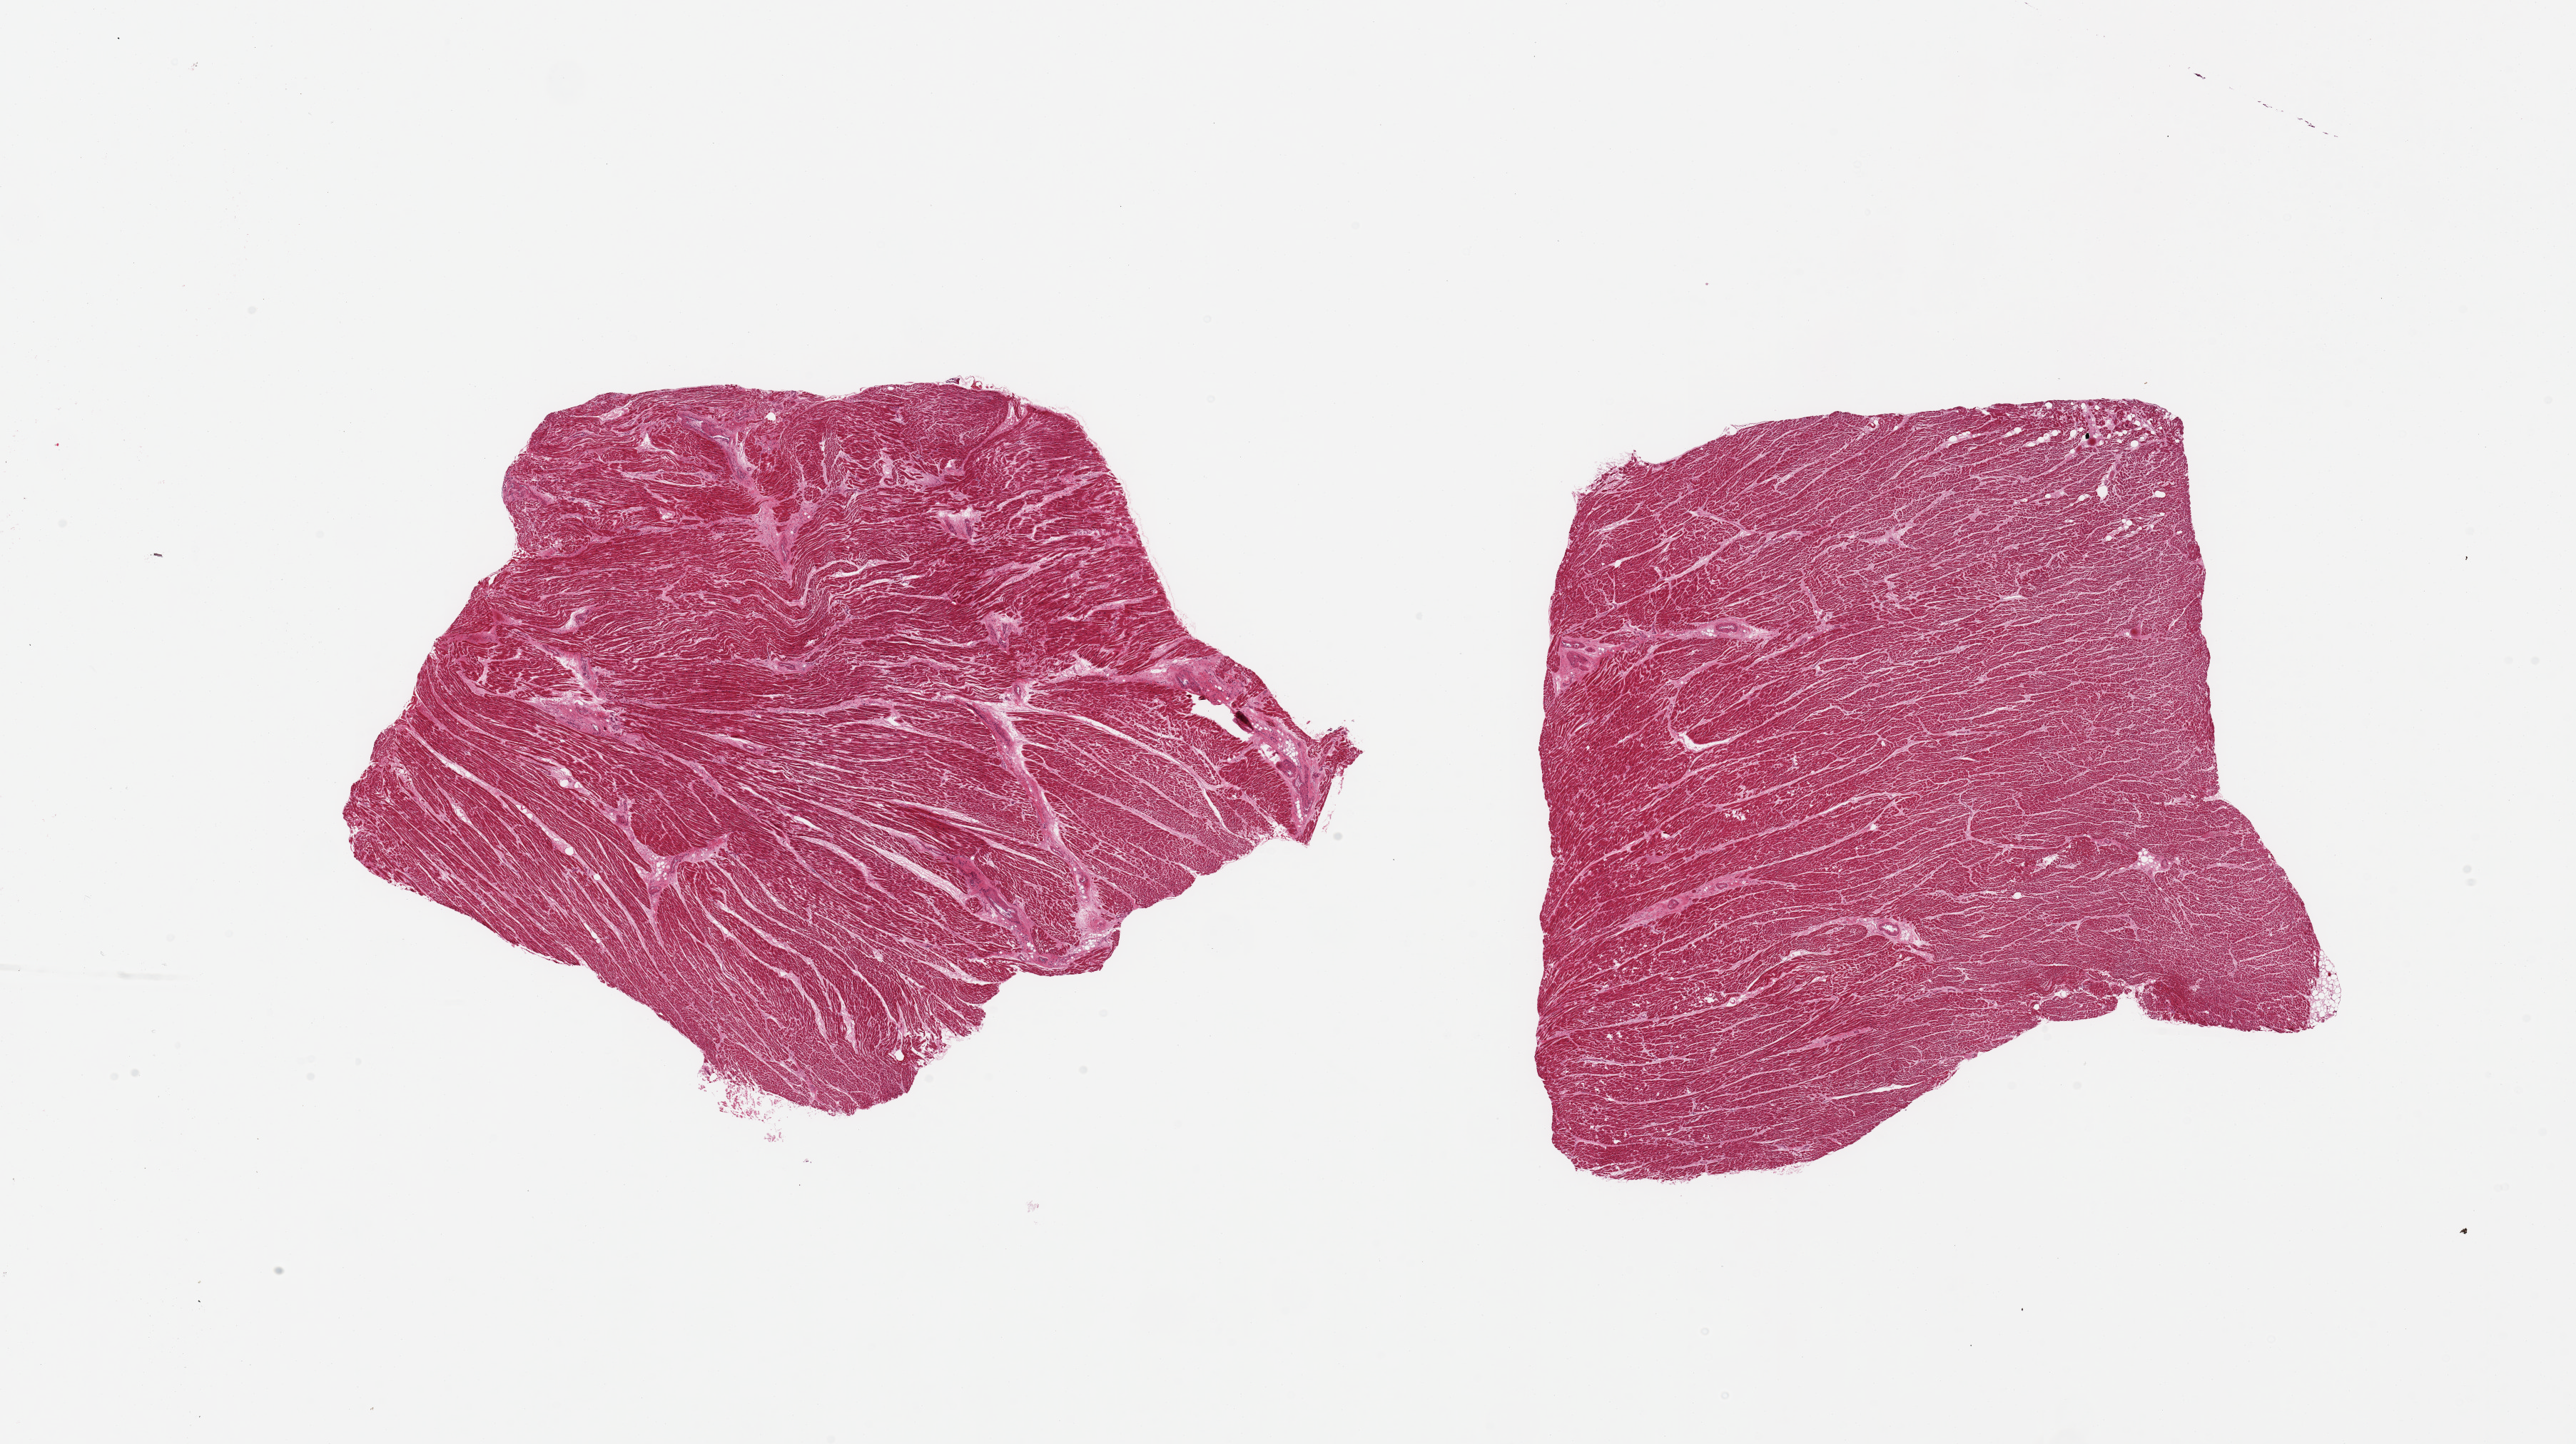
Haematoxylin and eosin whole-slide image — whole scanned area (about 28.5 x 16.0 mm, acquisition: 20x scan) shown as a low-resolution overview, PAXgene-fixed, paraffin-embedded tissue, section of heart (target tissue), donor tissue sample. Donor sex: male.
• pathologist's review note for this sample: 2 pieces; mild to moderate autolysis; interstitial fibrosis; focal fatty infiltration; trace of adherent fat